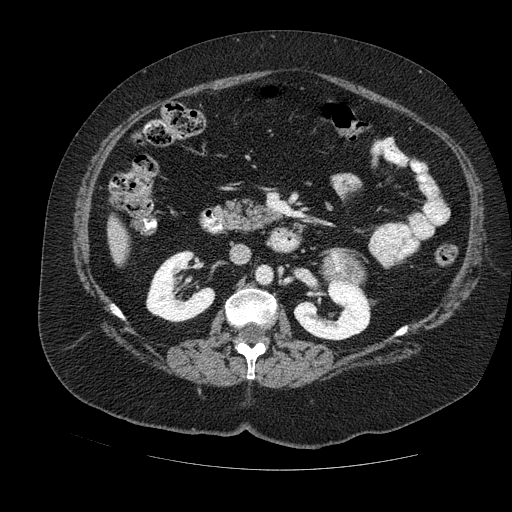
Contrast-enhanced abdominal CT, one axial slice; slice 55 of 121 in the series (ordered by position); soft-tissue window (W 400 / L 40 HU); 2.5 mm slice thickness; 512 × 512 image matrix, field of view 420 × 420 mm. Female patient. From the clinical record (not read from this slice): diagnosis: adrenocortical carcinoma; tumour side: left adrenal; tumour size at pathology: 8 cm; Ki-67 index: 7 %; stage (as recorded): 2.
Annotated regions visible in this slice (semi-automatically segmented with operator editing):
- mass: bounding box [x1, y1, x2, y2] px = [323, 252, 363, 280]